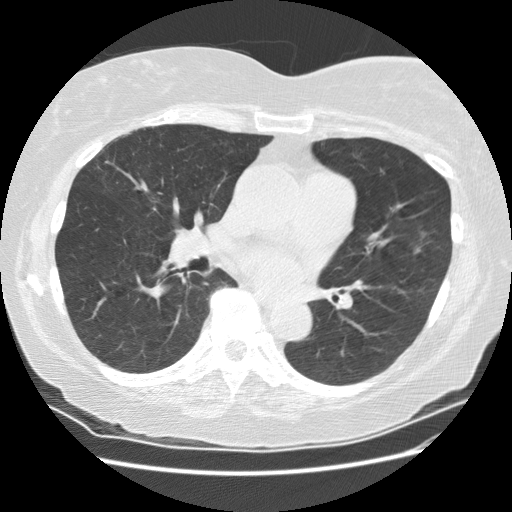
Axial slice from a low-dose chest CT screening exam, second annual screen, lung window (W 1500 / L -600 HU), 2.5 mm slice thickness, standard (soft-tissue) reconstruction kernel (STANDARD), slice 94 of 180 in the series. Female, age 71 years at enrolment. Former smoker at enrolment.
Expert-annotated lung lesion, box from (x=392, y=223) to (x=442, y=261) px. The exam's reader record, not a measurement of the box and not confirmed to be the same lesion: non-calcified nodule or mass ≥4 mm, lingula, 13 × 13 mm, poorly defined margins, ground glass attenuation, pre-existing on the prior screen: yes; interval growth: yes. Lung cancer was diagnosed 26 days after this screen: adenocarcinoma, NOS, left upper lobe, well differentiated (G1), stage IA (AJCC 6th edition), 11 mm at pathology.